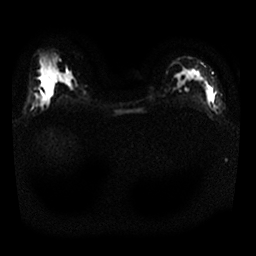
Breast MRI, one axial slice; slice 17 of 25 in the series (ordered by position); diffusion-weighted series; image 2 of 4 stored at this slice position (different b-values; order by instance number); 1.5 T; 4 mm slice thickness; 256 × 256 image matrix. Female patient.
Annotated regions visible in this slice (manually delineated by an expert):
- tumour on diffusion-weighted imaging: box from (x=207, y=88) to (x=214, y=100) px